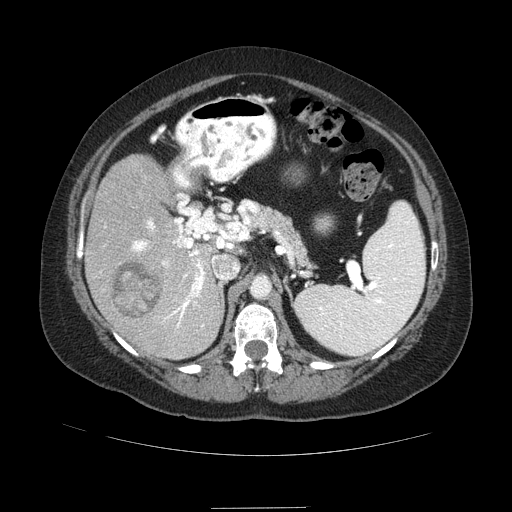
Contrast-enhanced abdominal CT (liver protocol), one axial slice; slice 48 of 89 in the series (ordered by position); soft-tissue window (W 400 / L 40 HU); 512 × 512 image matrix, field of view 400 × 400 mm. Case-level facts recorded for this patient, not image findings: diagnosis: hepatocellular carcinoma (patient treated with transarterial chemoembolisation; whether this scan precedes or follows treatment is not stated here); TNM stage (as recorded): Stage-IIIB; Child-Pugh class: A.
Structures marked on this image (semi-automatic segmentation, software-assisted and operator-edited):
- liver parenchyma outside the tumour (the mass and vessels are separate outlines, so this box may not span the whole liver): bounding box <86,154,226,359> (left, top, right, bottom; pixels)
- mass: <110,258,163,319>
- liver vessels: <132,220,226,328>